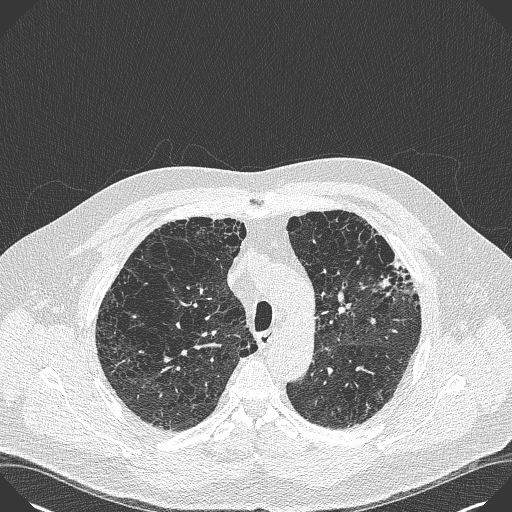
Low-dose screening chest CT, axial slice. Baseline screening round. Lung window (W 1500 / L -600 HU). Lung (sharp) reconstruction kernel (B50f). Slice 110 of 383 in the series. Male, age 59 years at enrolment. Current smoker at enrolment.
Expert reader's lesion annotation, bounding box <373,251,430,302> (left, top, right, bottom; pixels). Screening reader's record for this exam: no non-calcified nodule ≥4 mm recorded. Official screen result: negative screen, minor abnormalities not suspicious for lung cancer.